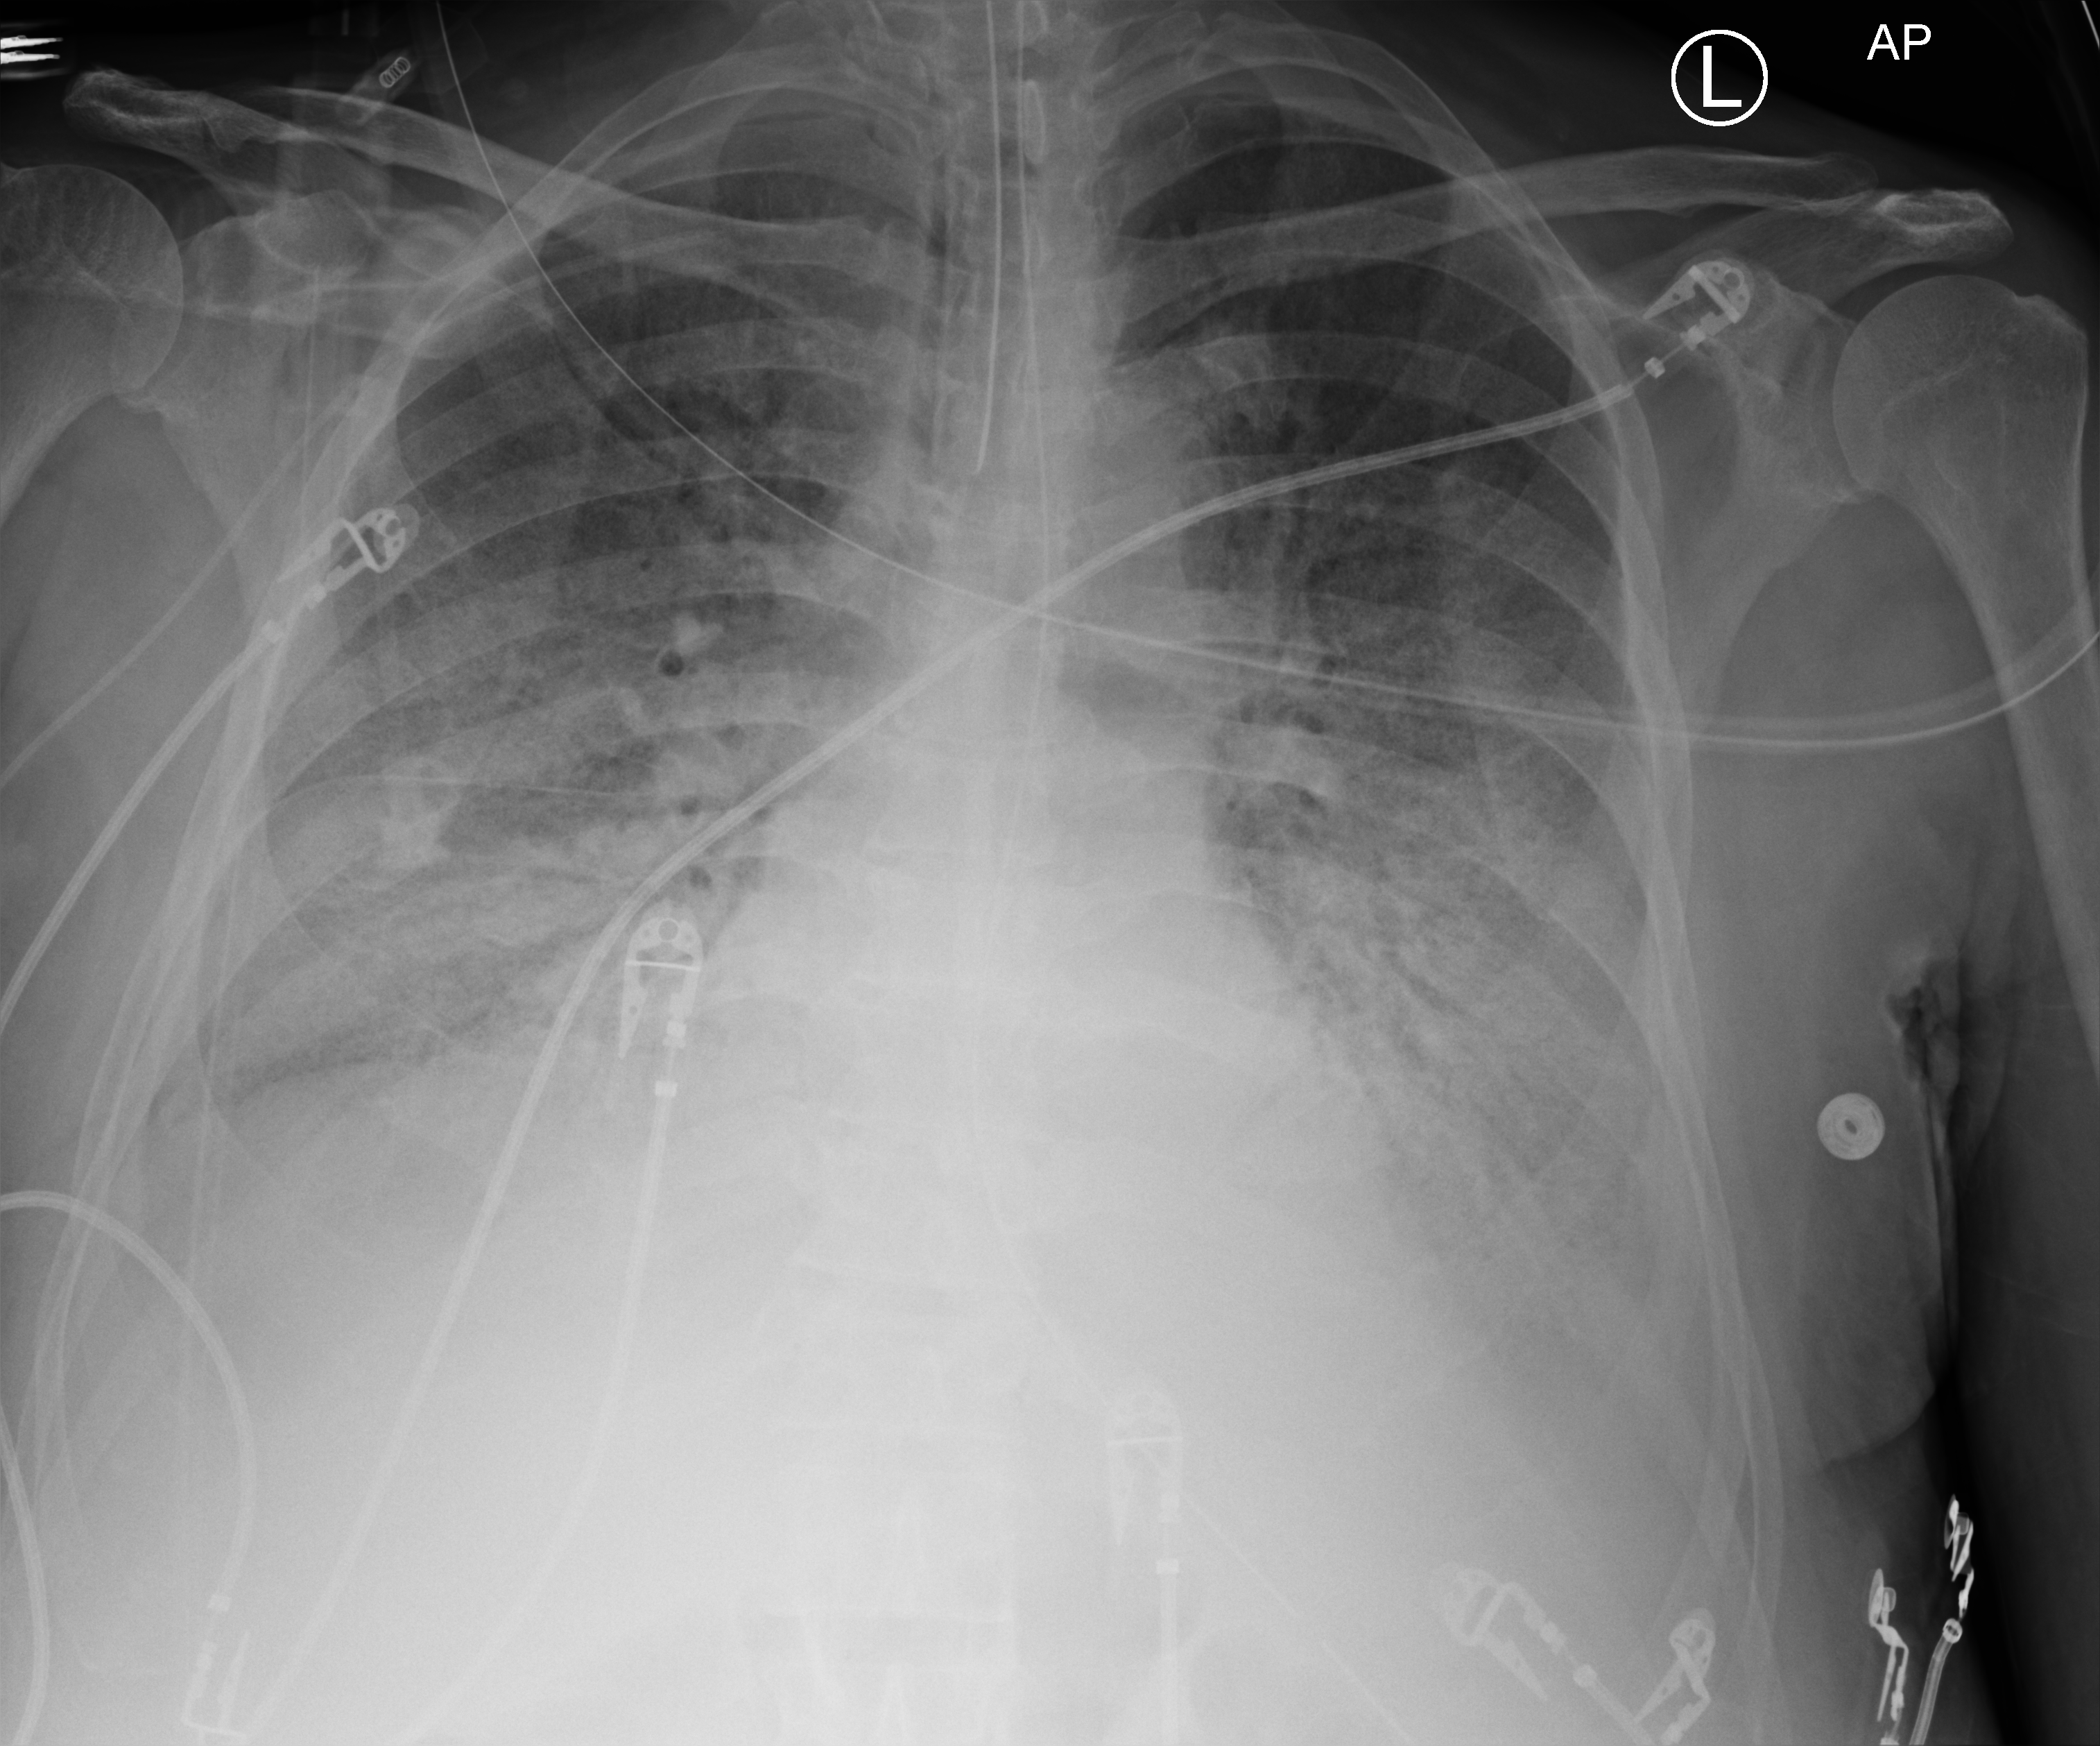
Bedside chest radiograph (computed radiography), anteroposterior (AP) projection. Male patient hospitalised with COVID-19, age 60–74 years.
Admission-level facts for this patient (not findings on this image; timing relative to this image not recorded): length of hospital stay: 24 days; admitted to intensive care during this hospital stay: yes.